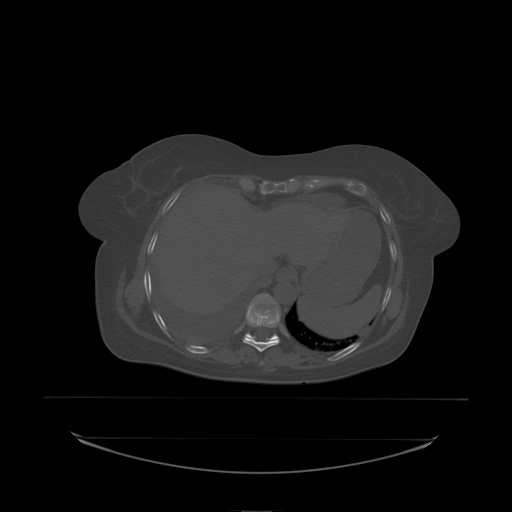
CT including the spine, one axial slice; slice 121 of 242 in the series (ordered by position); bone window (W 1800 / L 400 HU); 2.5 mm slice thickness; 512 × 512 image matrix. Patient: female, 53 years. From the clinical record (not read from this slice): primary cancer: lung; vertebrae with lytic lesions (as recorded): T7, L1.
Annotated regions visible in this slice (semi-automatic segmentation, software-assisted and operator-edited):
- T10 vertebra: bounding box <245,294,280,338> (left, top, right, bottom; pixels)
- T9 vertebra: <246,306,281,328>